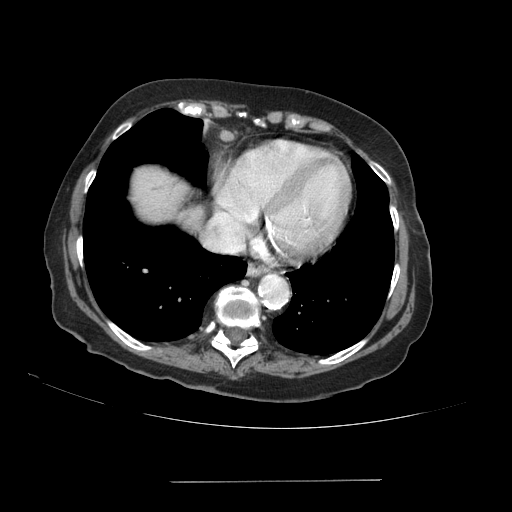
Contrast-enhanced abdominal CT (liver protocol), one axial slice. Position 83 of 89 along the scan axis. Reconstruction kernel STANDARD. 140 kVp. Soft-tissue window (W 400 / L 40 HU). 2.5 mm slice thickness. 512 × 512 image matrix. From the clinical record (not read from this slice): diagnosis: hepatocellular carcinoma (patient treated with transarterial chemoembolisation; whether this scan precedes or follows treatment is not stated here); TNM stage (as recorded): Stage-IVA; Child-Pugh class: A; tumour differentiation: poorly differentiated; tumour nodularity: uninodular.
Annotated regions visible in this slice (semi-automatic segmentation, software-assisted and operator-edited):
- liver parenchyma outside the tumour (the mass and vessels are separate outlines, so this box may not span the whole liver): bounding box (x1, y1, x2, y2) in pixels: (132, 166, 188, 222)